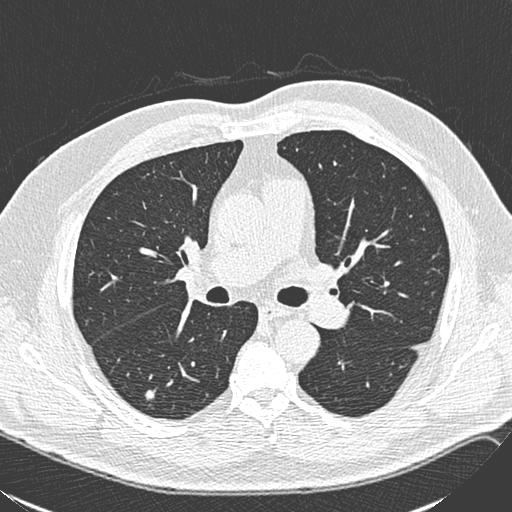
Low-dose screening chest CT, one axial slice. Position 154 of 248 along the scan axis. Lung window (W 1500 / L -600 HU). 512 × 512 image matrix, field of view 357 × 357 mm.
Structures marked on this image (outlined manually by an expert reader):
- lesion 1 (tumor, lower lobe of right lung): bounding box [x1, y1, x2, y2] px = [145, 390, 155, 400]